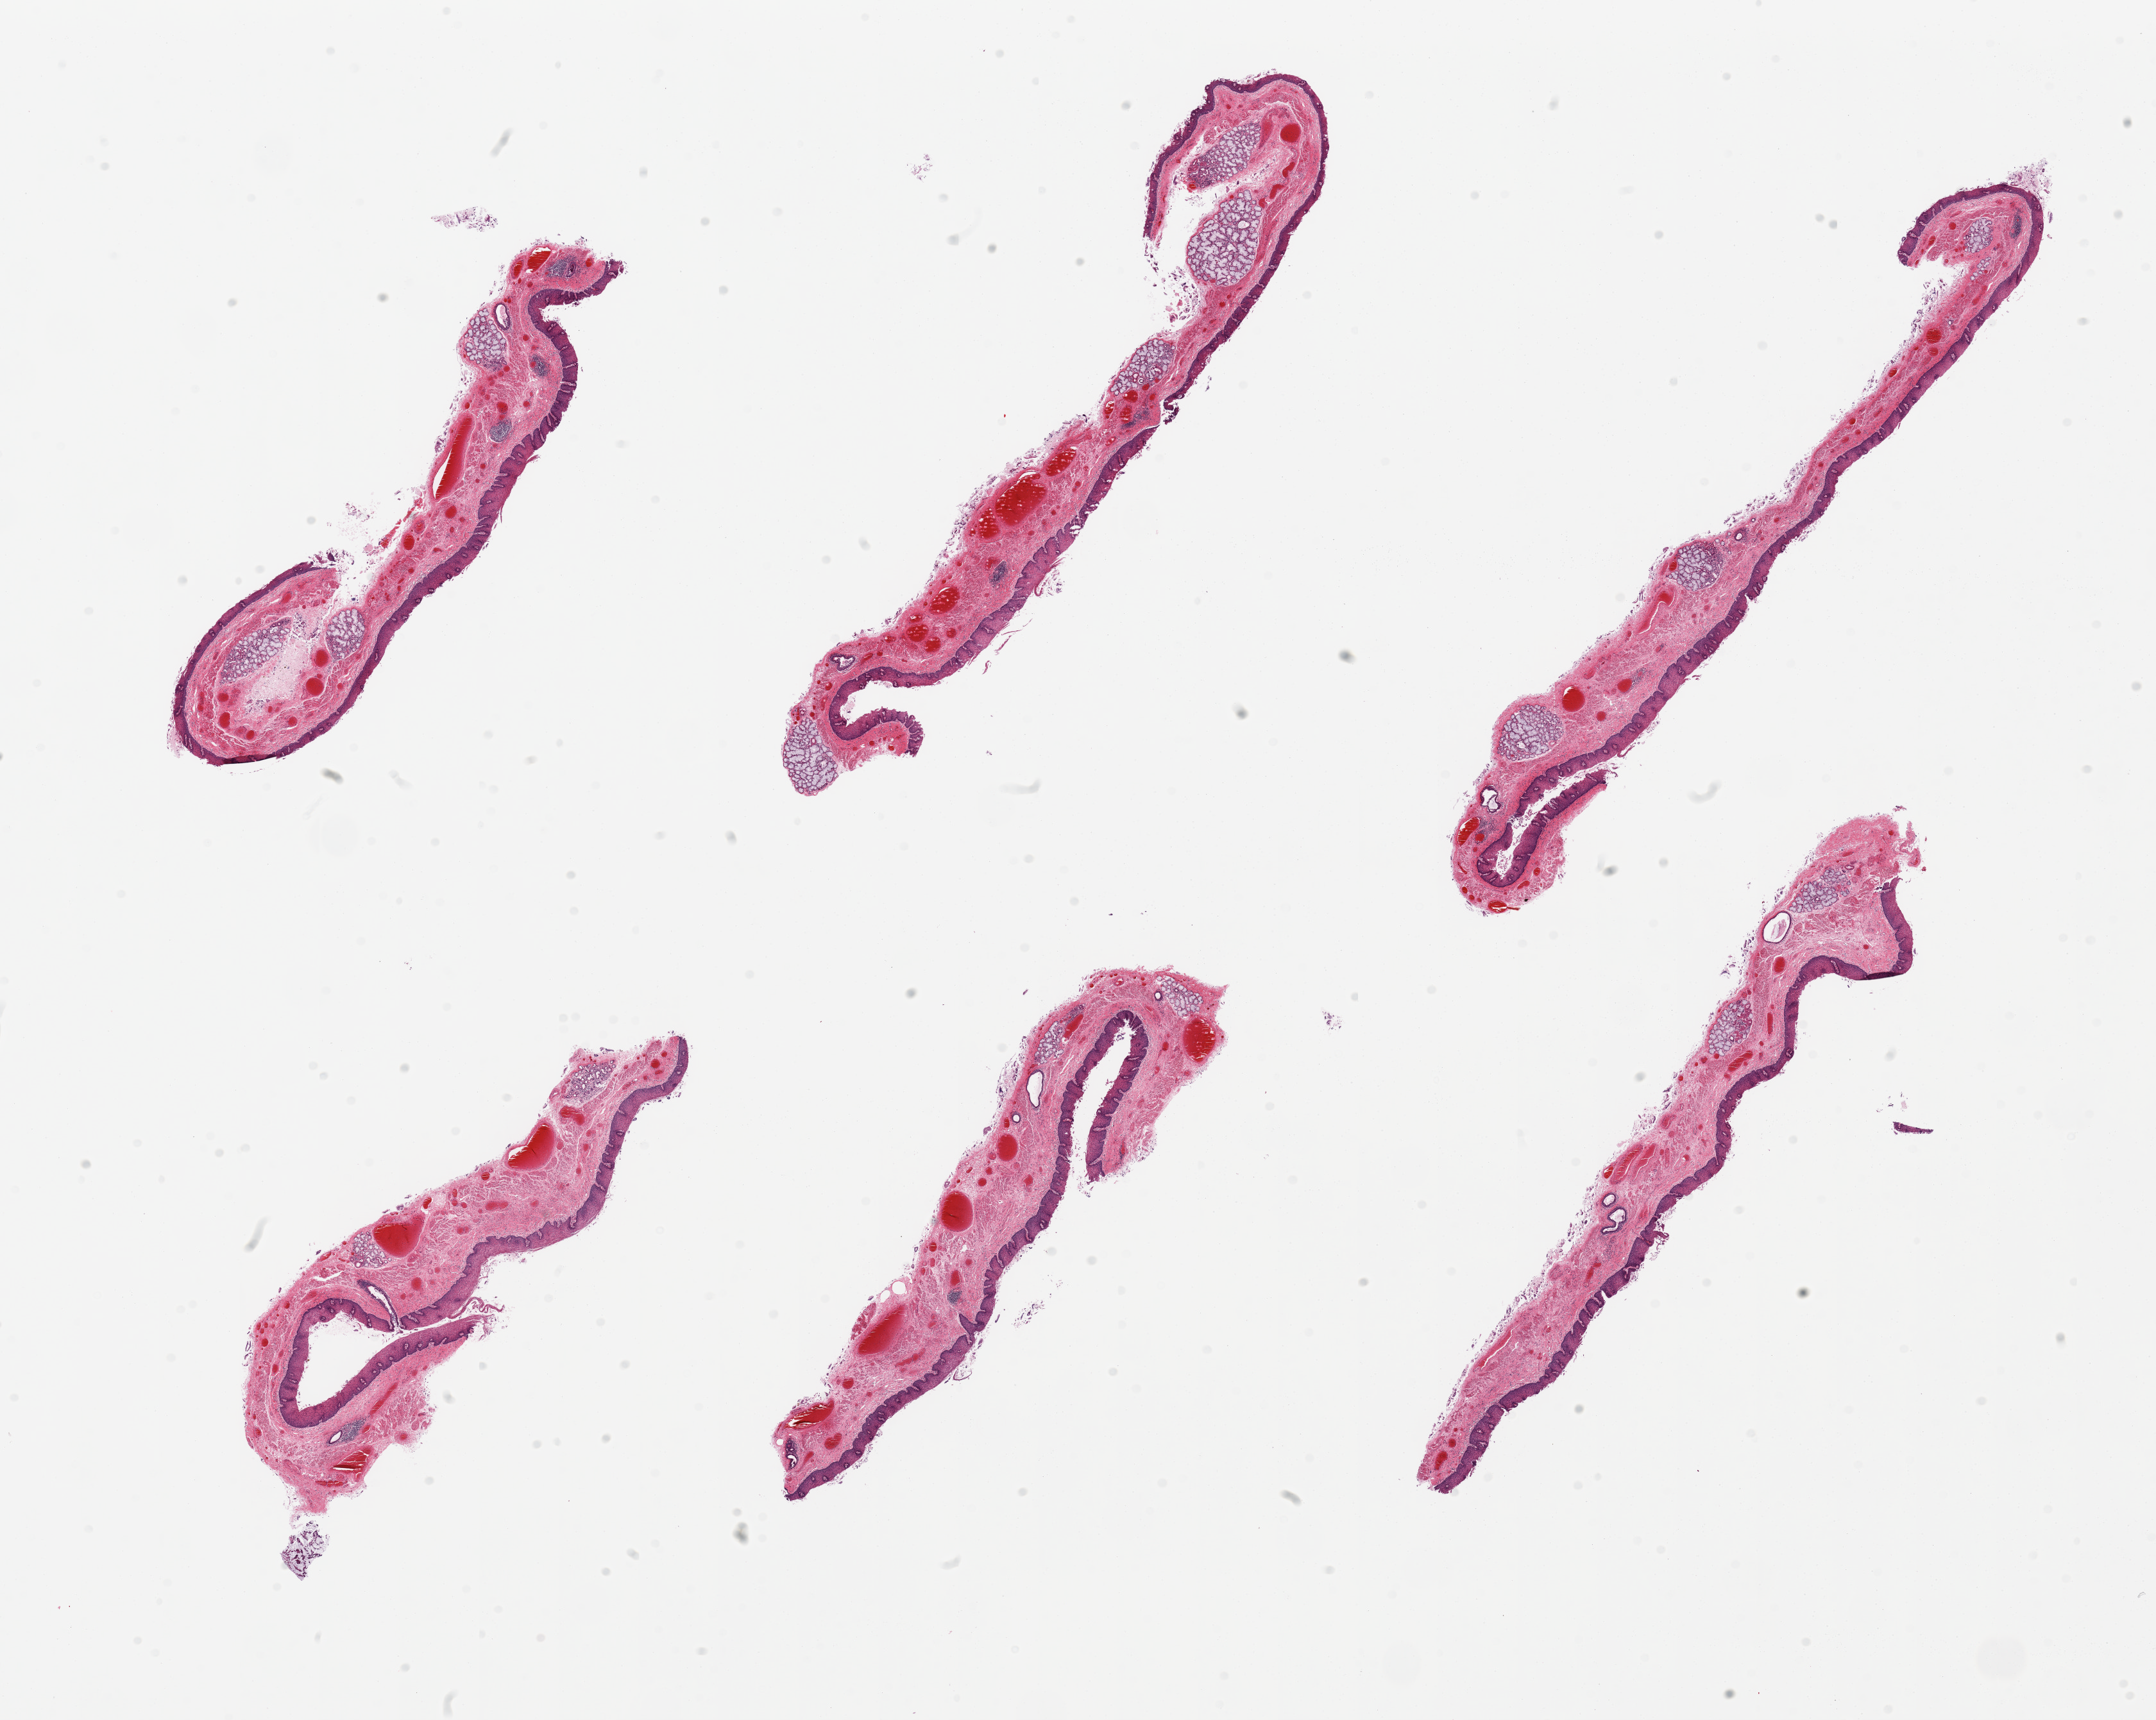
Whole-slide image, hematoxylin and eosin (H&E) stain — a low-resolution overview of the entire scanned area, about 26.6 x 21.2 mm. PAXgene-fixed paraffin-embedded (PFPE) section. Sampled site (target tissue): esophageal mucous membrane. Donor tissue sample. Donor: female.
Pathologist's review note for this sample: 6 pieces, well trimmed mucosa.